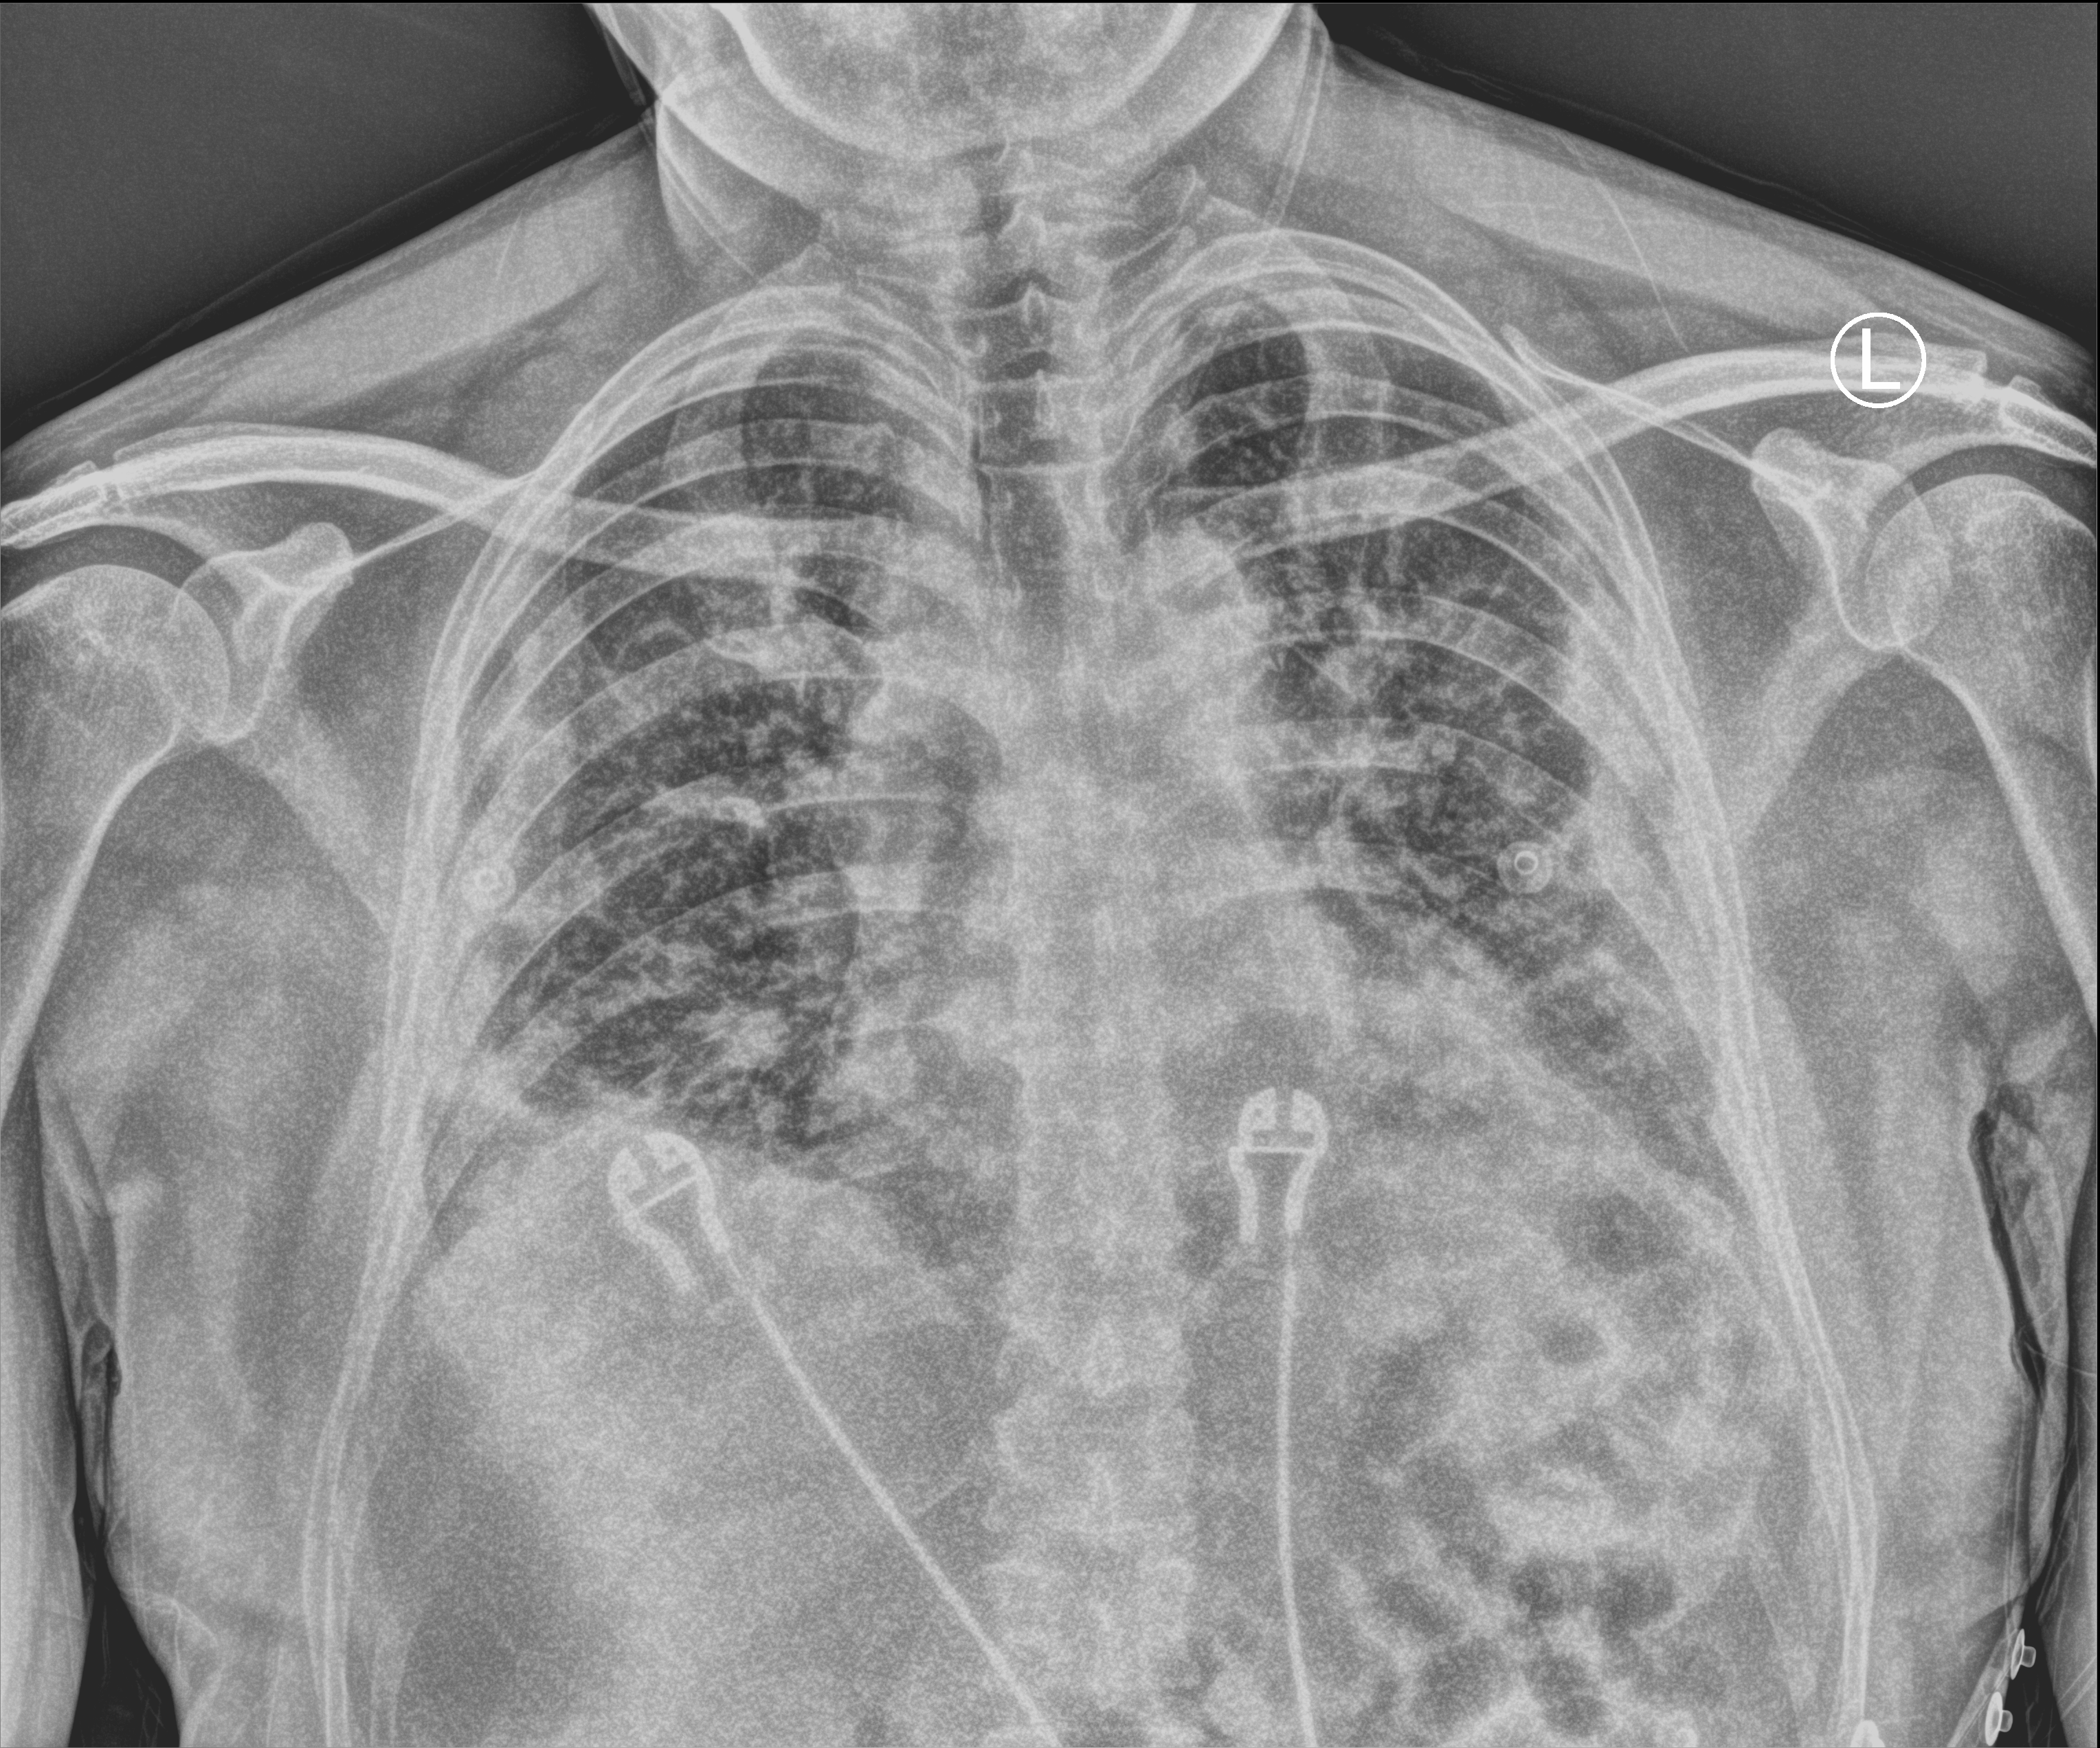
Portable chest radiograph; anteroposterior (AP) projection. Patient hospitalised with COVID-19; male, aged 18–59 years.
Hospital-stay facts (about this admission, not read from this image; timing relative to this image not recorded): admitted to intensive care during this hospital stay: no; smoking status (admission record): never.